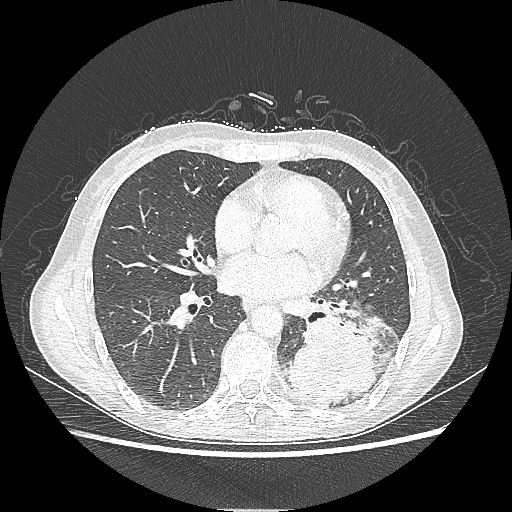
Chest CT, one axial slice; position 102 of 220 along the scan axis; reconstruction kernel LUNG; 80 kVp; lung window (W 1500 / L -600 HU); 512 × 512 image matrix. Female patient, age 53 years. Case-level facts recorded for this patient, not image findings: clinical TNM (as recorded): T3 N0 M0.
Annotated regions visible in this slice (rectangle marked by the reading radiologist):
- lung tumour (recorded histology: adenocarcinoma): bounding box [x1, y1, x2, y2] px = [287, 307, 380, 407]